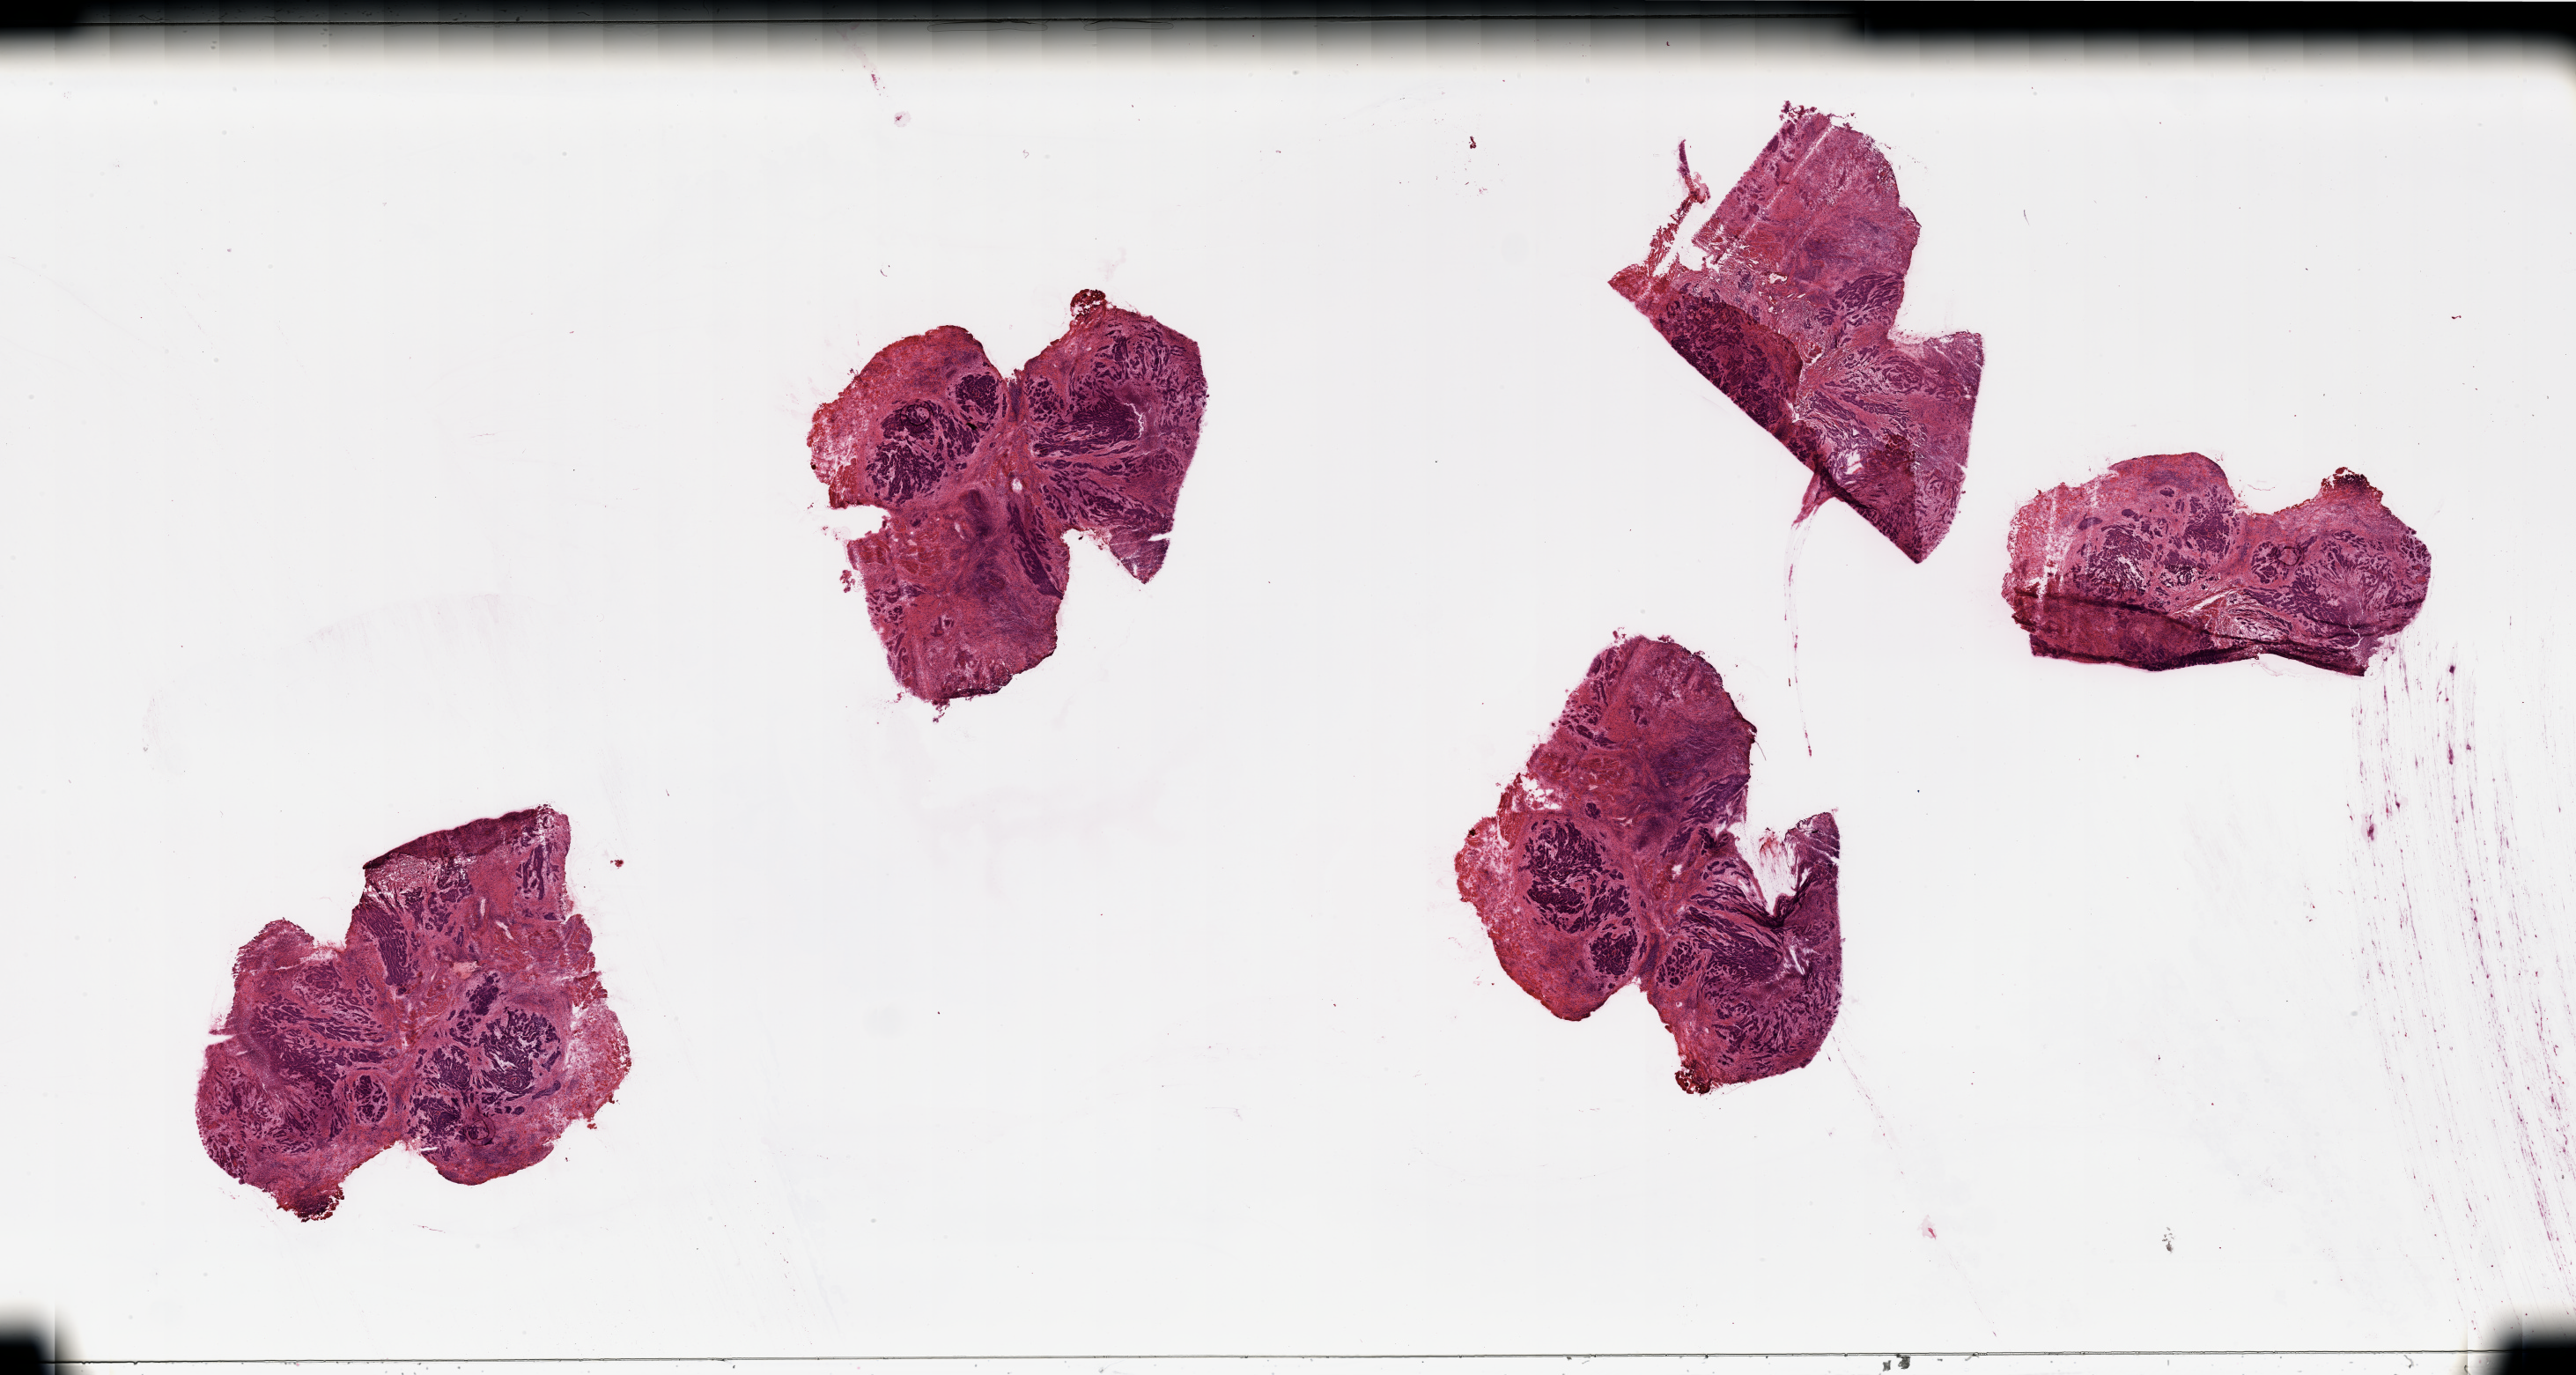
H&E-stained whole-slide image, low-resolution overview of the scanned area, about 46.3 x 24.7 mm (acquisition: 20x scan). Tumour tissue sample, sampled site: tongue. Male, 53 y/o. Histologic grade: G2 (moderately differentiated). Pathologist review of this section (percent, as recorded): tumour nuclei 80%, necrosis 15%.
Primary tumour site (as recorded): oral cavity. Diagnosis: Squamous cell carcinoma, NOS (tongue, NOS). AJCC pathologic stage: IVA.